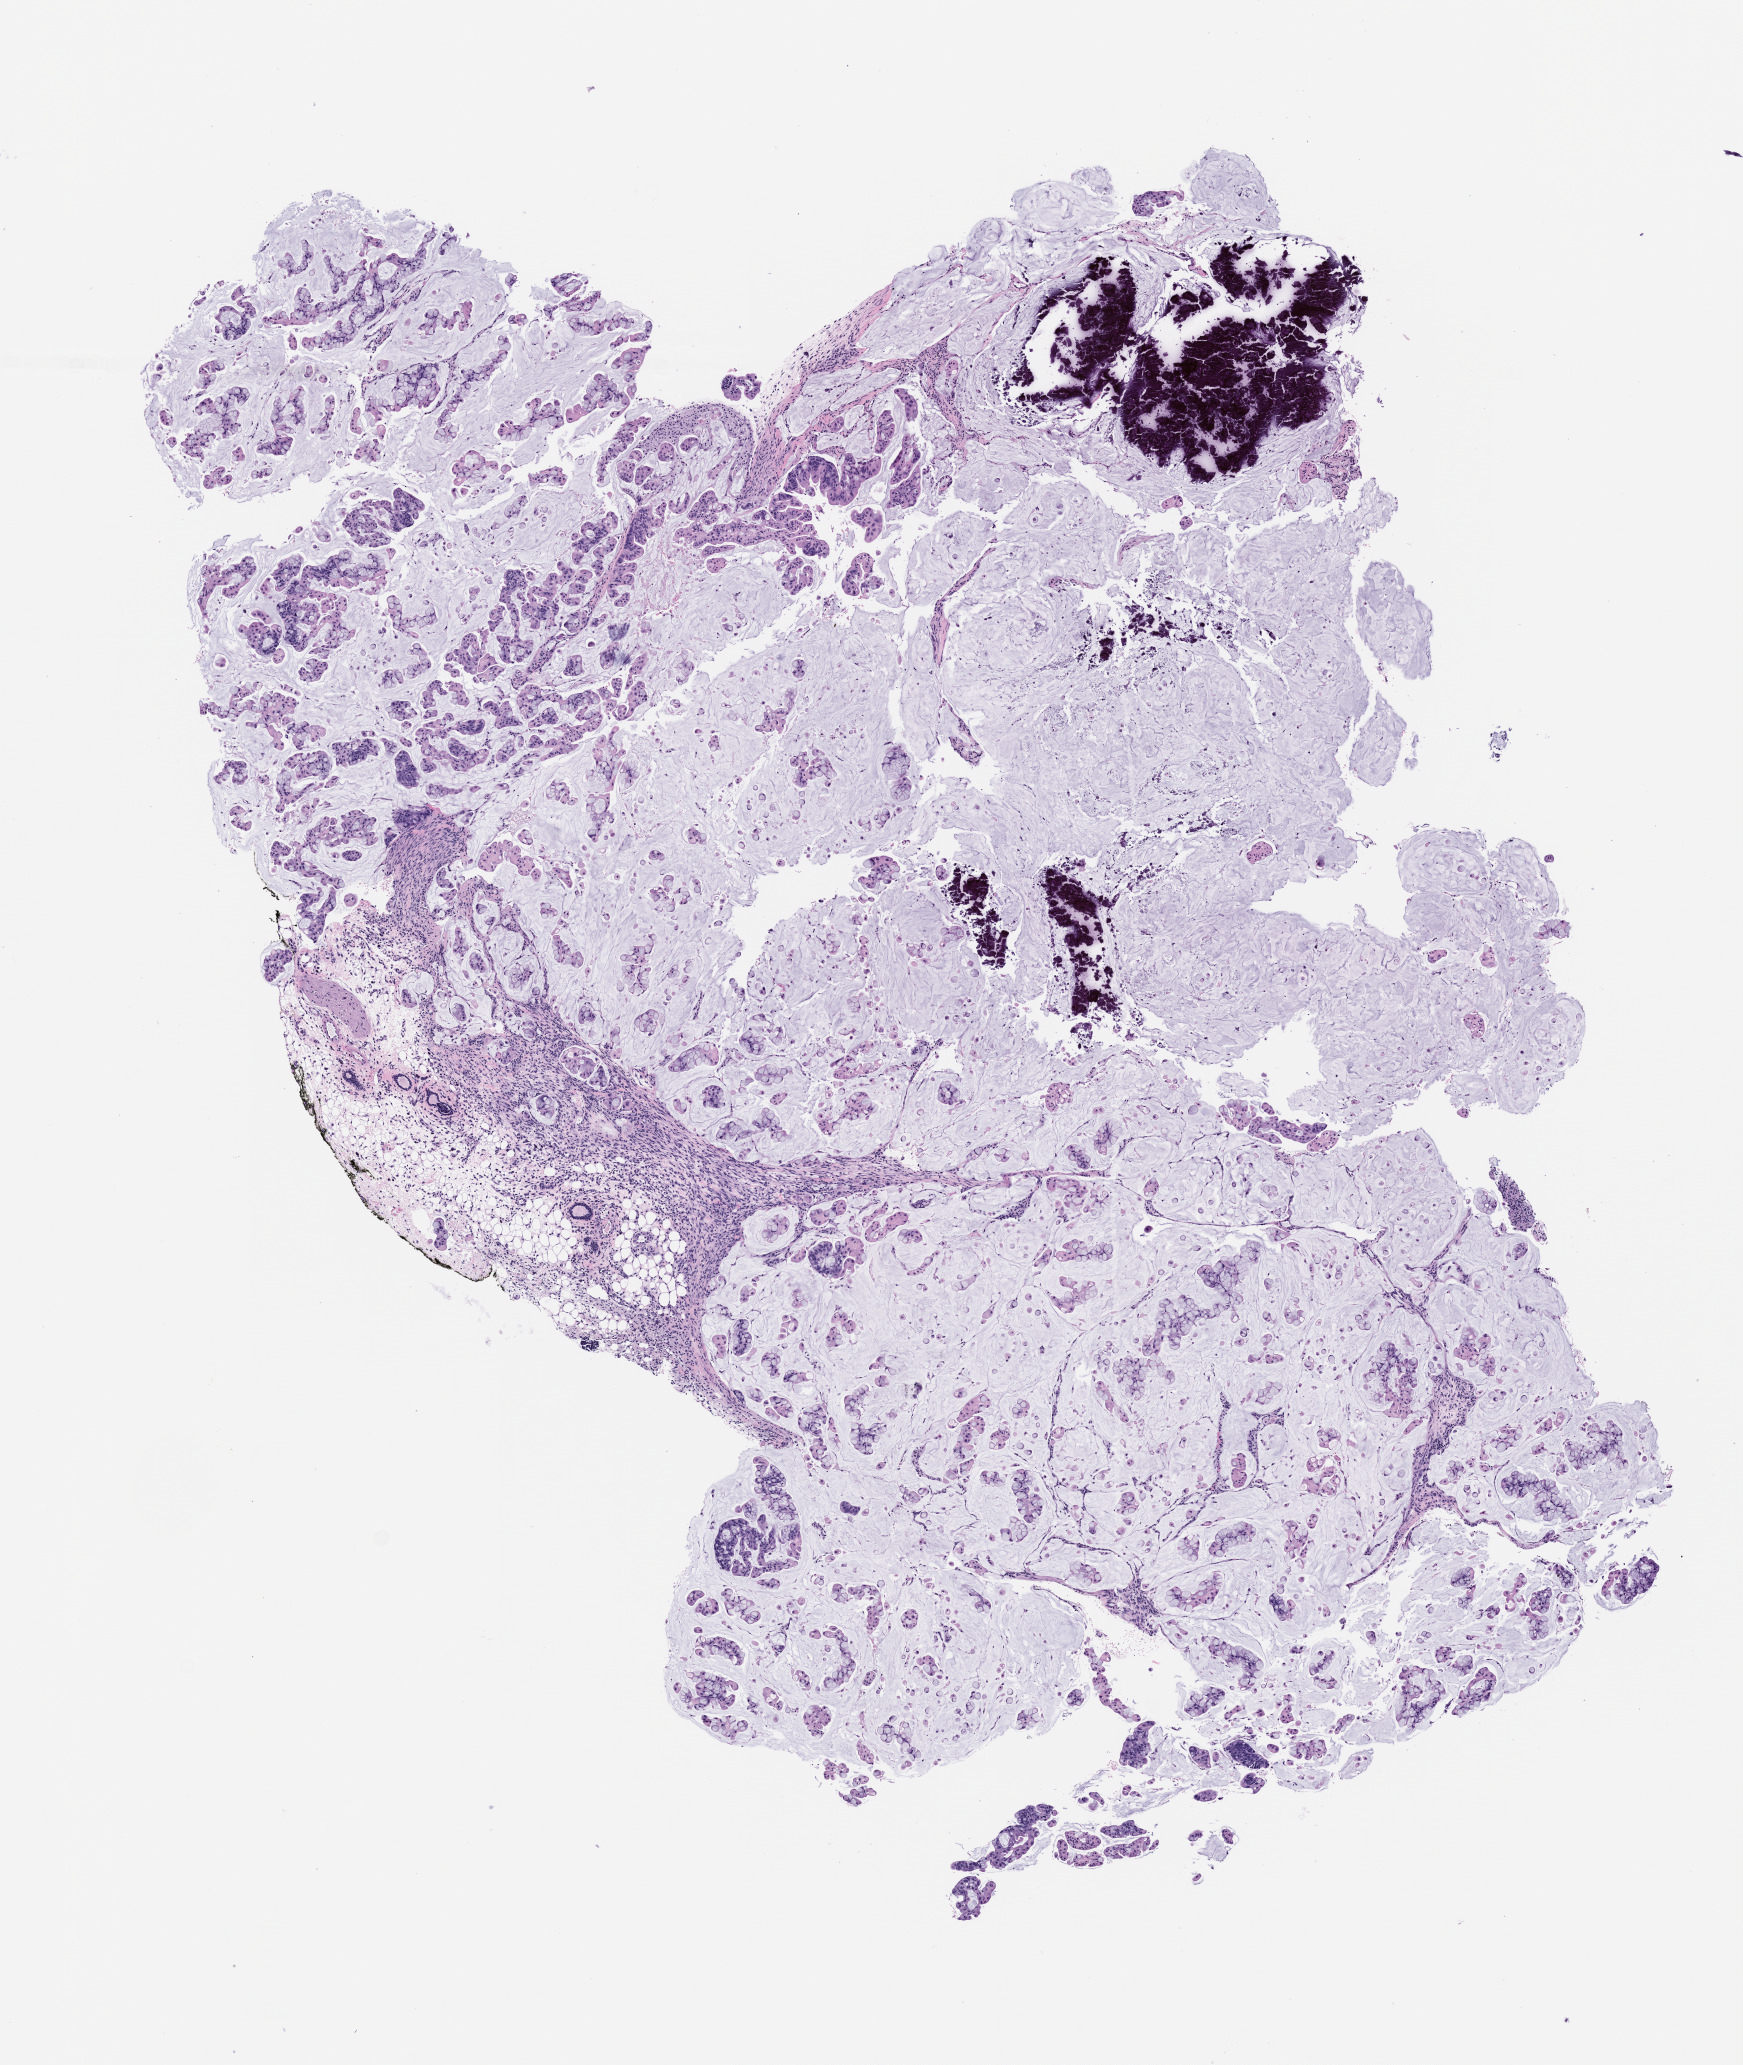
Whole-slide image, hematoxylin and eosin (H&E): patient-derived xenograft (human tumor grown in a mouse), passage 2, shown as a low-resolution overview of the whole scanned area (about 7.0 x 8.3 mm), formalin-fixed paraffin-embedded section, tumor site category: colon.
Originating patient diagnosis: Colon Adenocarcinoma.